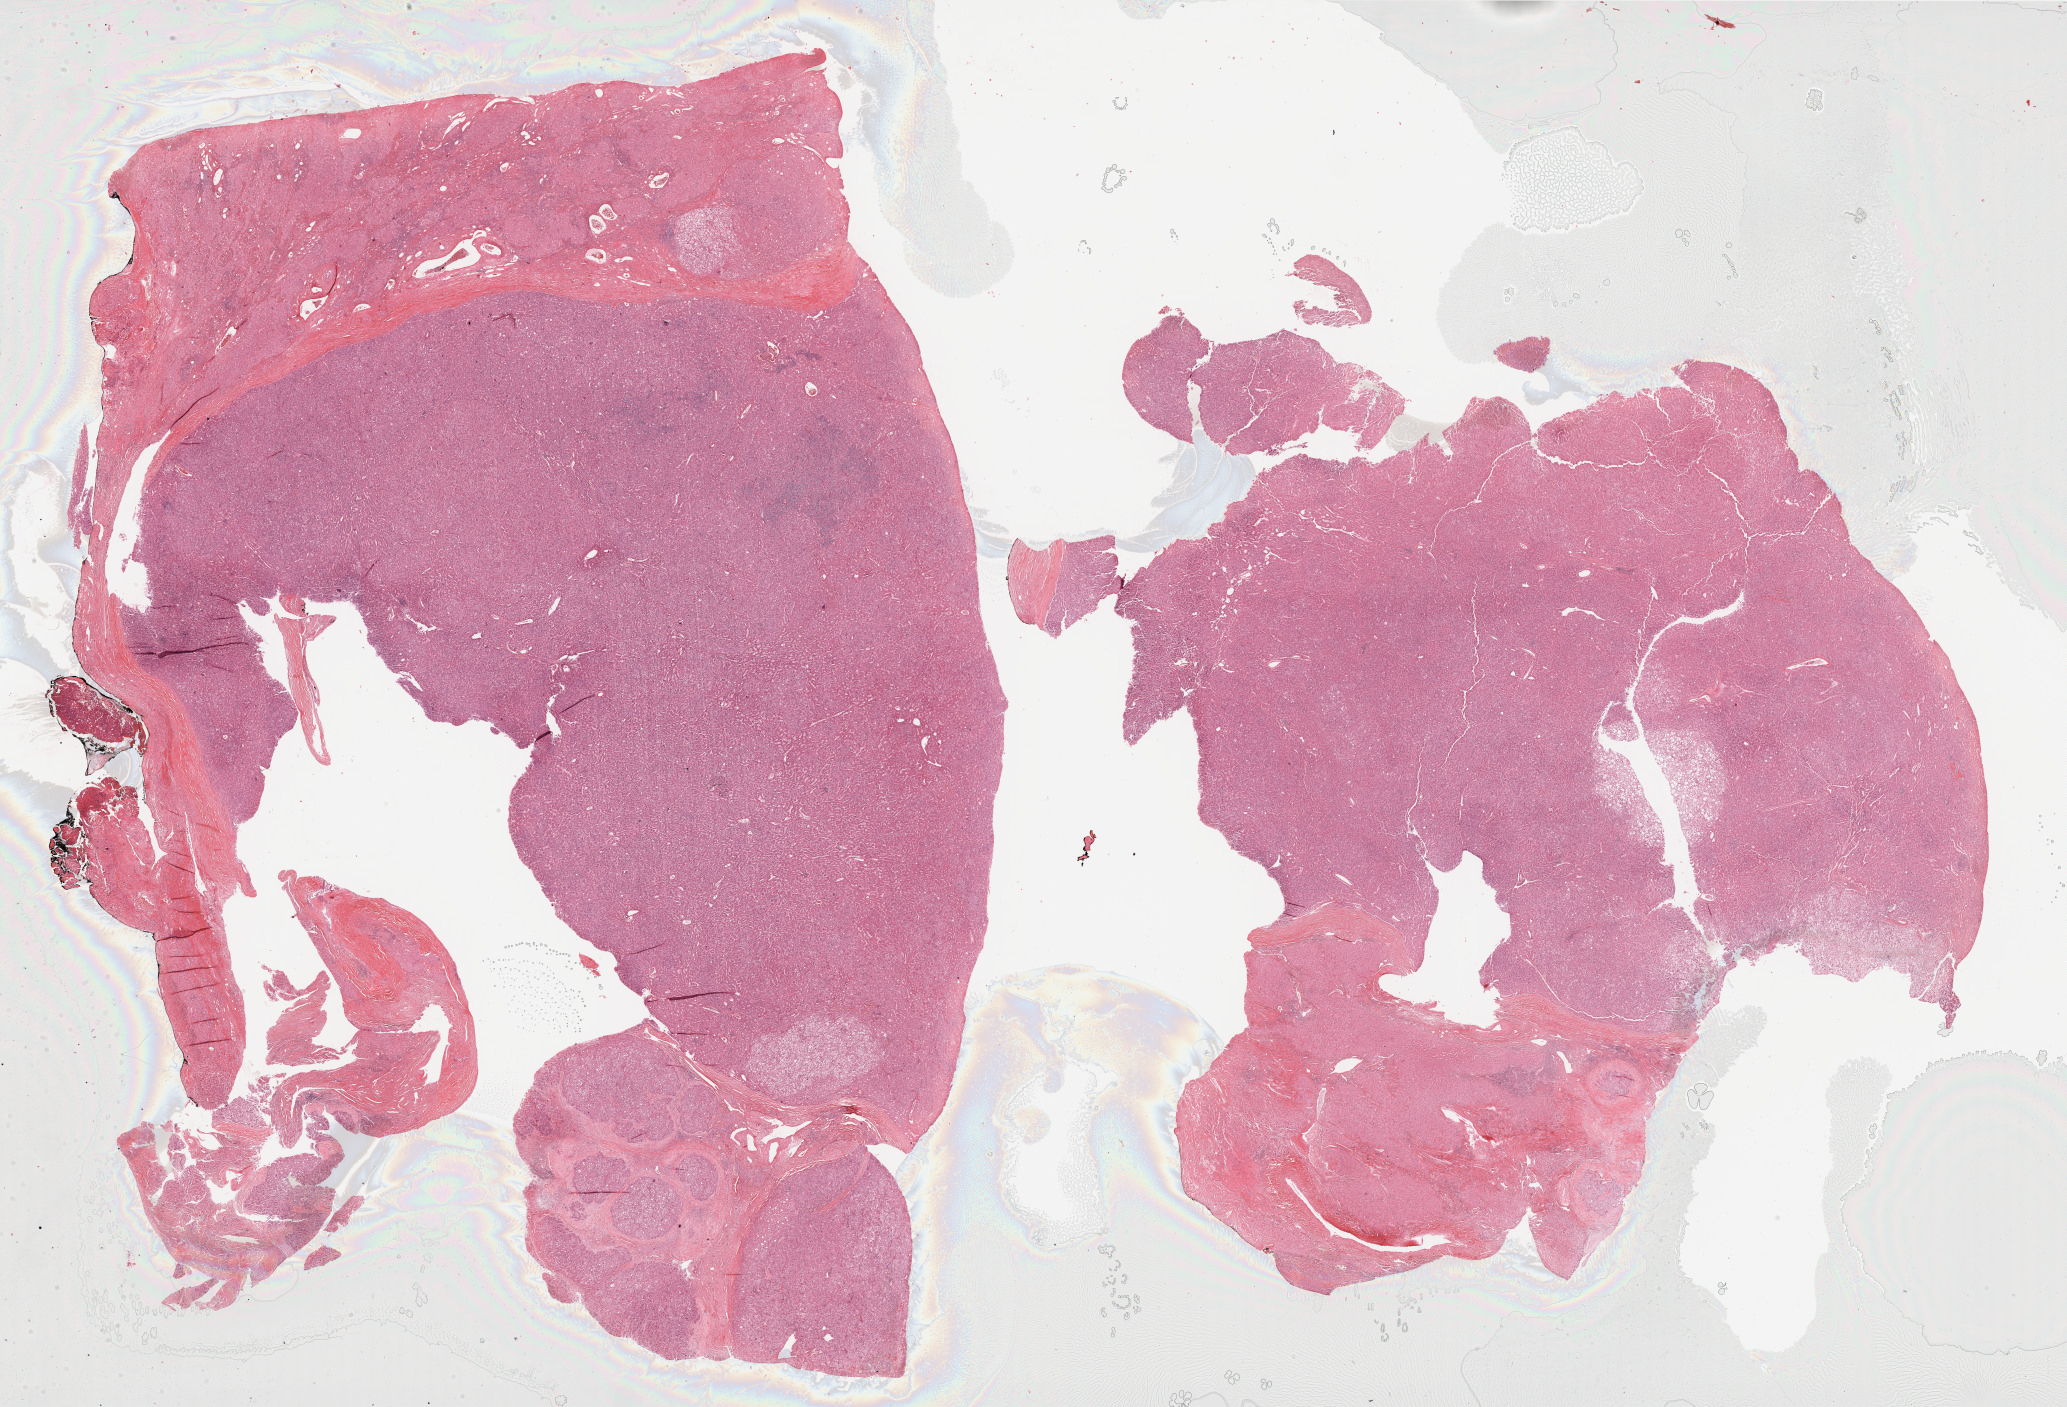
H&E-stained whole-slide image — whole scanned area (about 33.5 x 22.8 mm) shown as a low-resolution overview; formalin-fixed paraffin-embedded (FFPE) diagnostic section; primary tumour sample from the liver. Male, age 65 years at initial diagnosis. Histologic grade: G2 (moderately differentiated).
- diagnosis: Hepatocellular carcinoma, NOS
- AJCC pathologic stage: IIIA